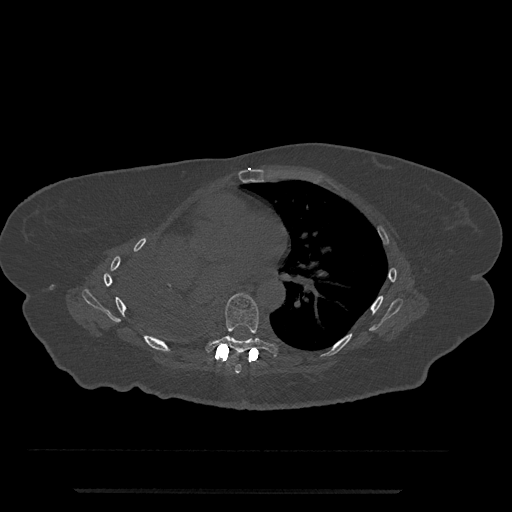
CT including the spine, one axial slice; position 446 of 797 along the scan axis; 120 kVp; bone window (W 1800 / L 400 HU); 0.5 mm slice thickness; 512 × 512 image matrix, field of view 440 × 440 mm. Patient: female, 51 years. From the clinical record (not read from this slice): primary cancer: neuro.
Structures marked on this image (semi-automatically segmented with operator editing):
- T6 vertebra: bounding box (x1, y1, x2, y2) in pixels: (234, 364, 241, 374)
- T7 vertebra: (205, 293, 279, 356)